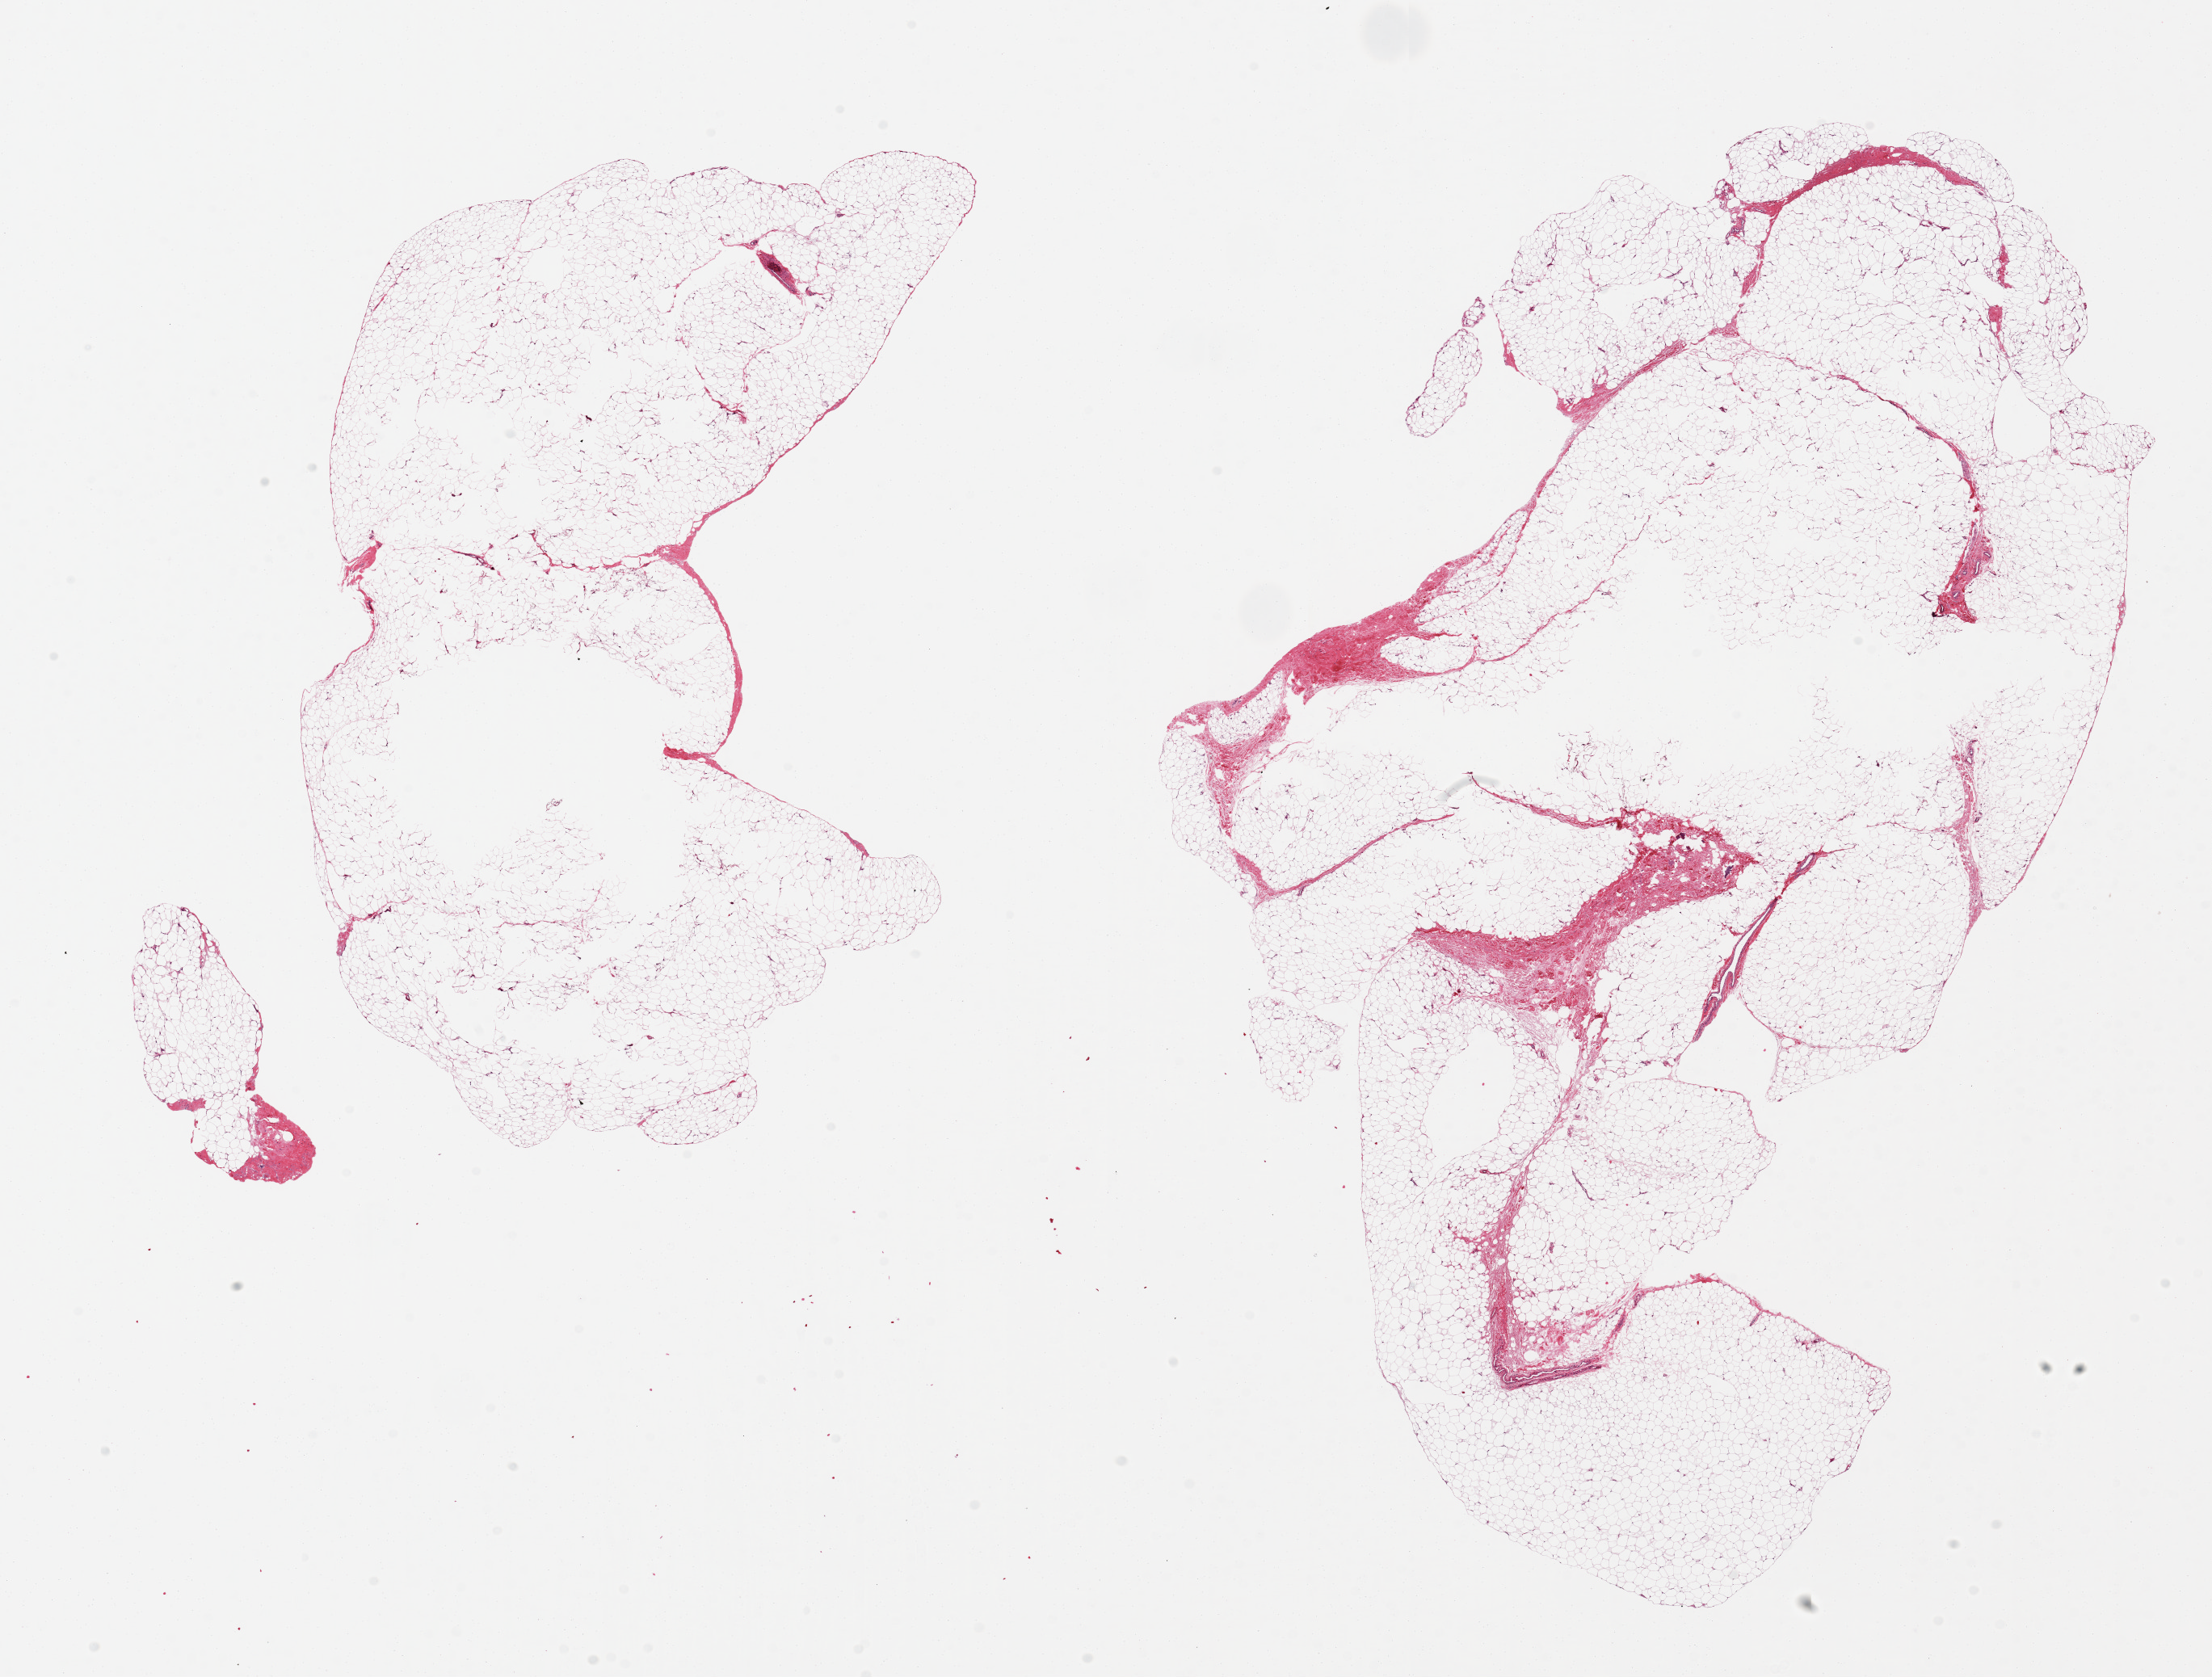
Hematoxylin and eosin (H&E) whole-slide image — low-resolution overview of the scanned area, about 21.7 x 16.4 mm; PAXgene-fixed, paraffin-embedded tissue; section of adipose tissue (target tissue); tissue donor sample.
• reviewer comment on this tissue sample: 2 pieces ~10x5mm